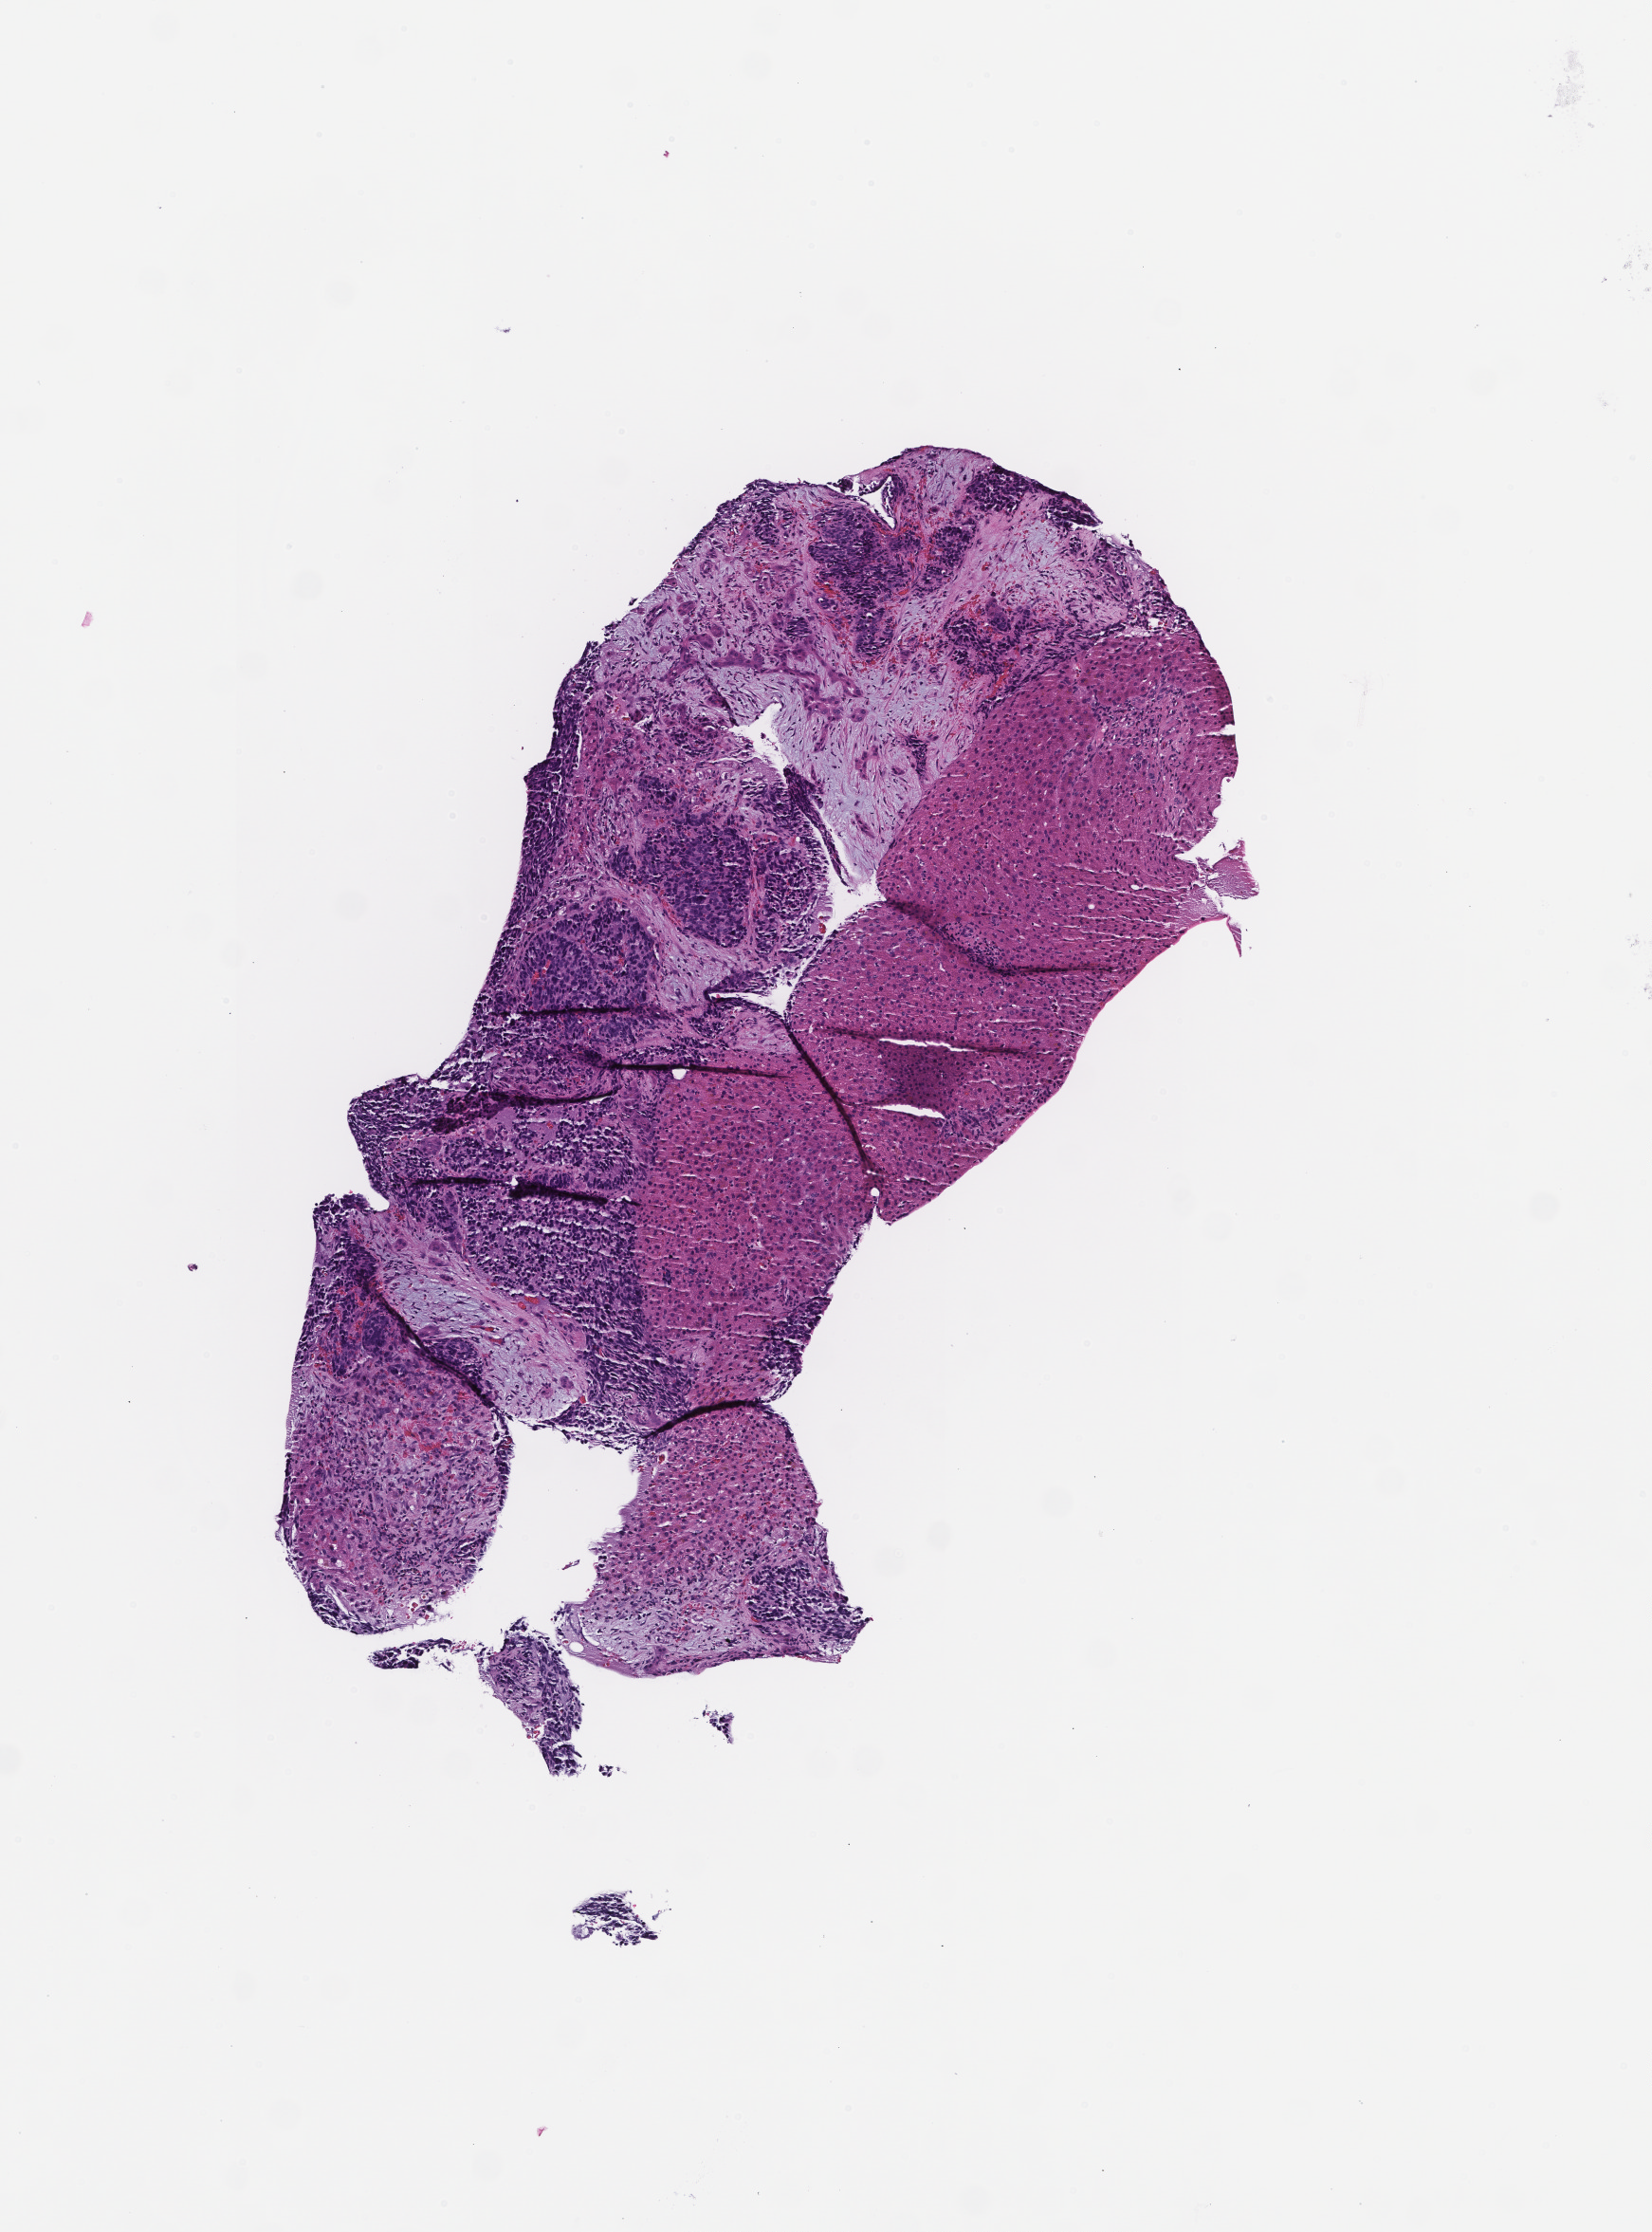
Digitized haematoxylin and eosin-stained section, a low-resolution overview of the entire scanned area, about 3.5 x 4.8 mm. Formalin-fixed, paraffin-embedded (FFPE) tissue. Specimen time point: collected at baseline (before treatment). Patient: female.
- this section: metastasis (sampled organ not recorded)
- patient diagnosis (primary): Non-Small Cell Lung Carcinoma